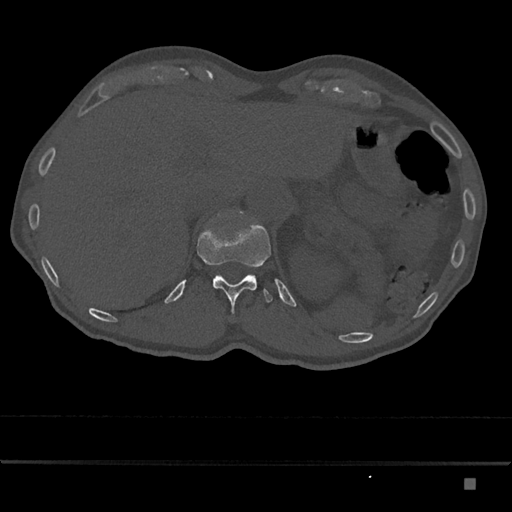
CT including the spine, one axial slice; slice 607 of 797 in the series (ordered by position); reconstruction kernel Br40s/3; bone window (W 1800 / L 400 HU); 0.5 mm slice thickness; 512 × 512 image matrix, field of view 390 × 390 mm. Male patient, age 72 years. Case-level facts recorded for this patient, not image findings: primary cancer: prostate.
Annotated regions visible in this slice (semi-automatically segmented with operator editing):
- T12 vertebra: box from (x=197, y=211) to (x=273, y=314) px